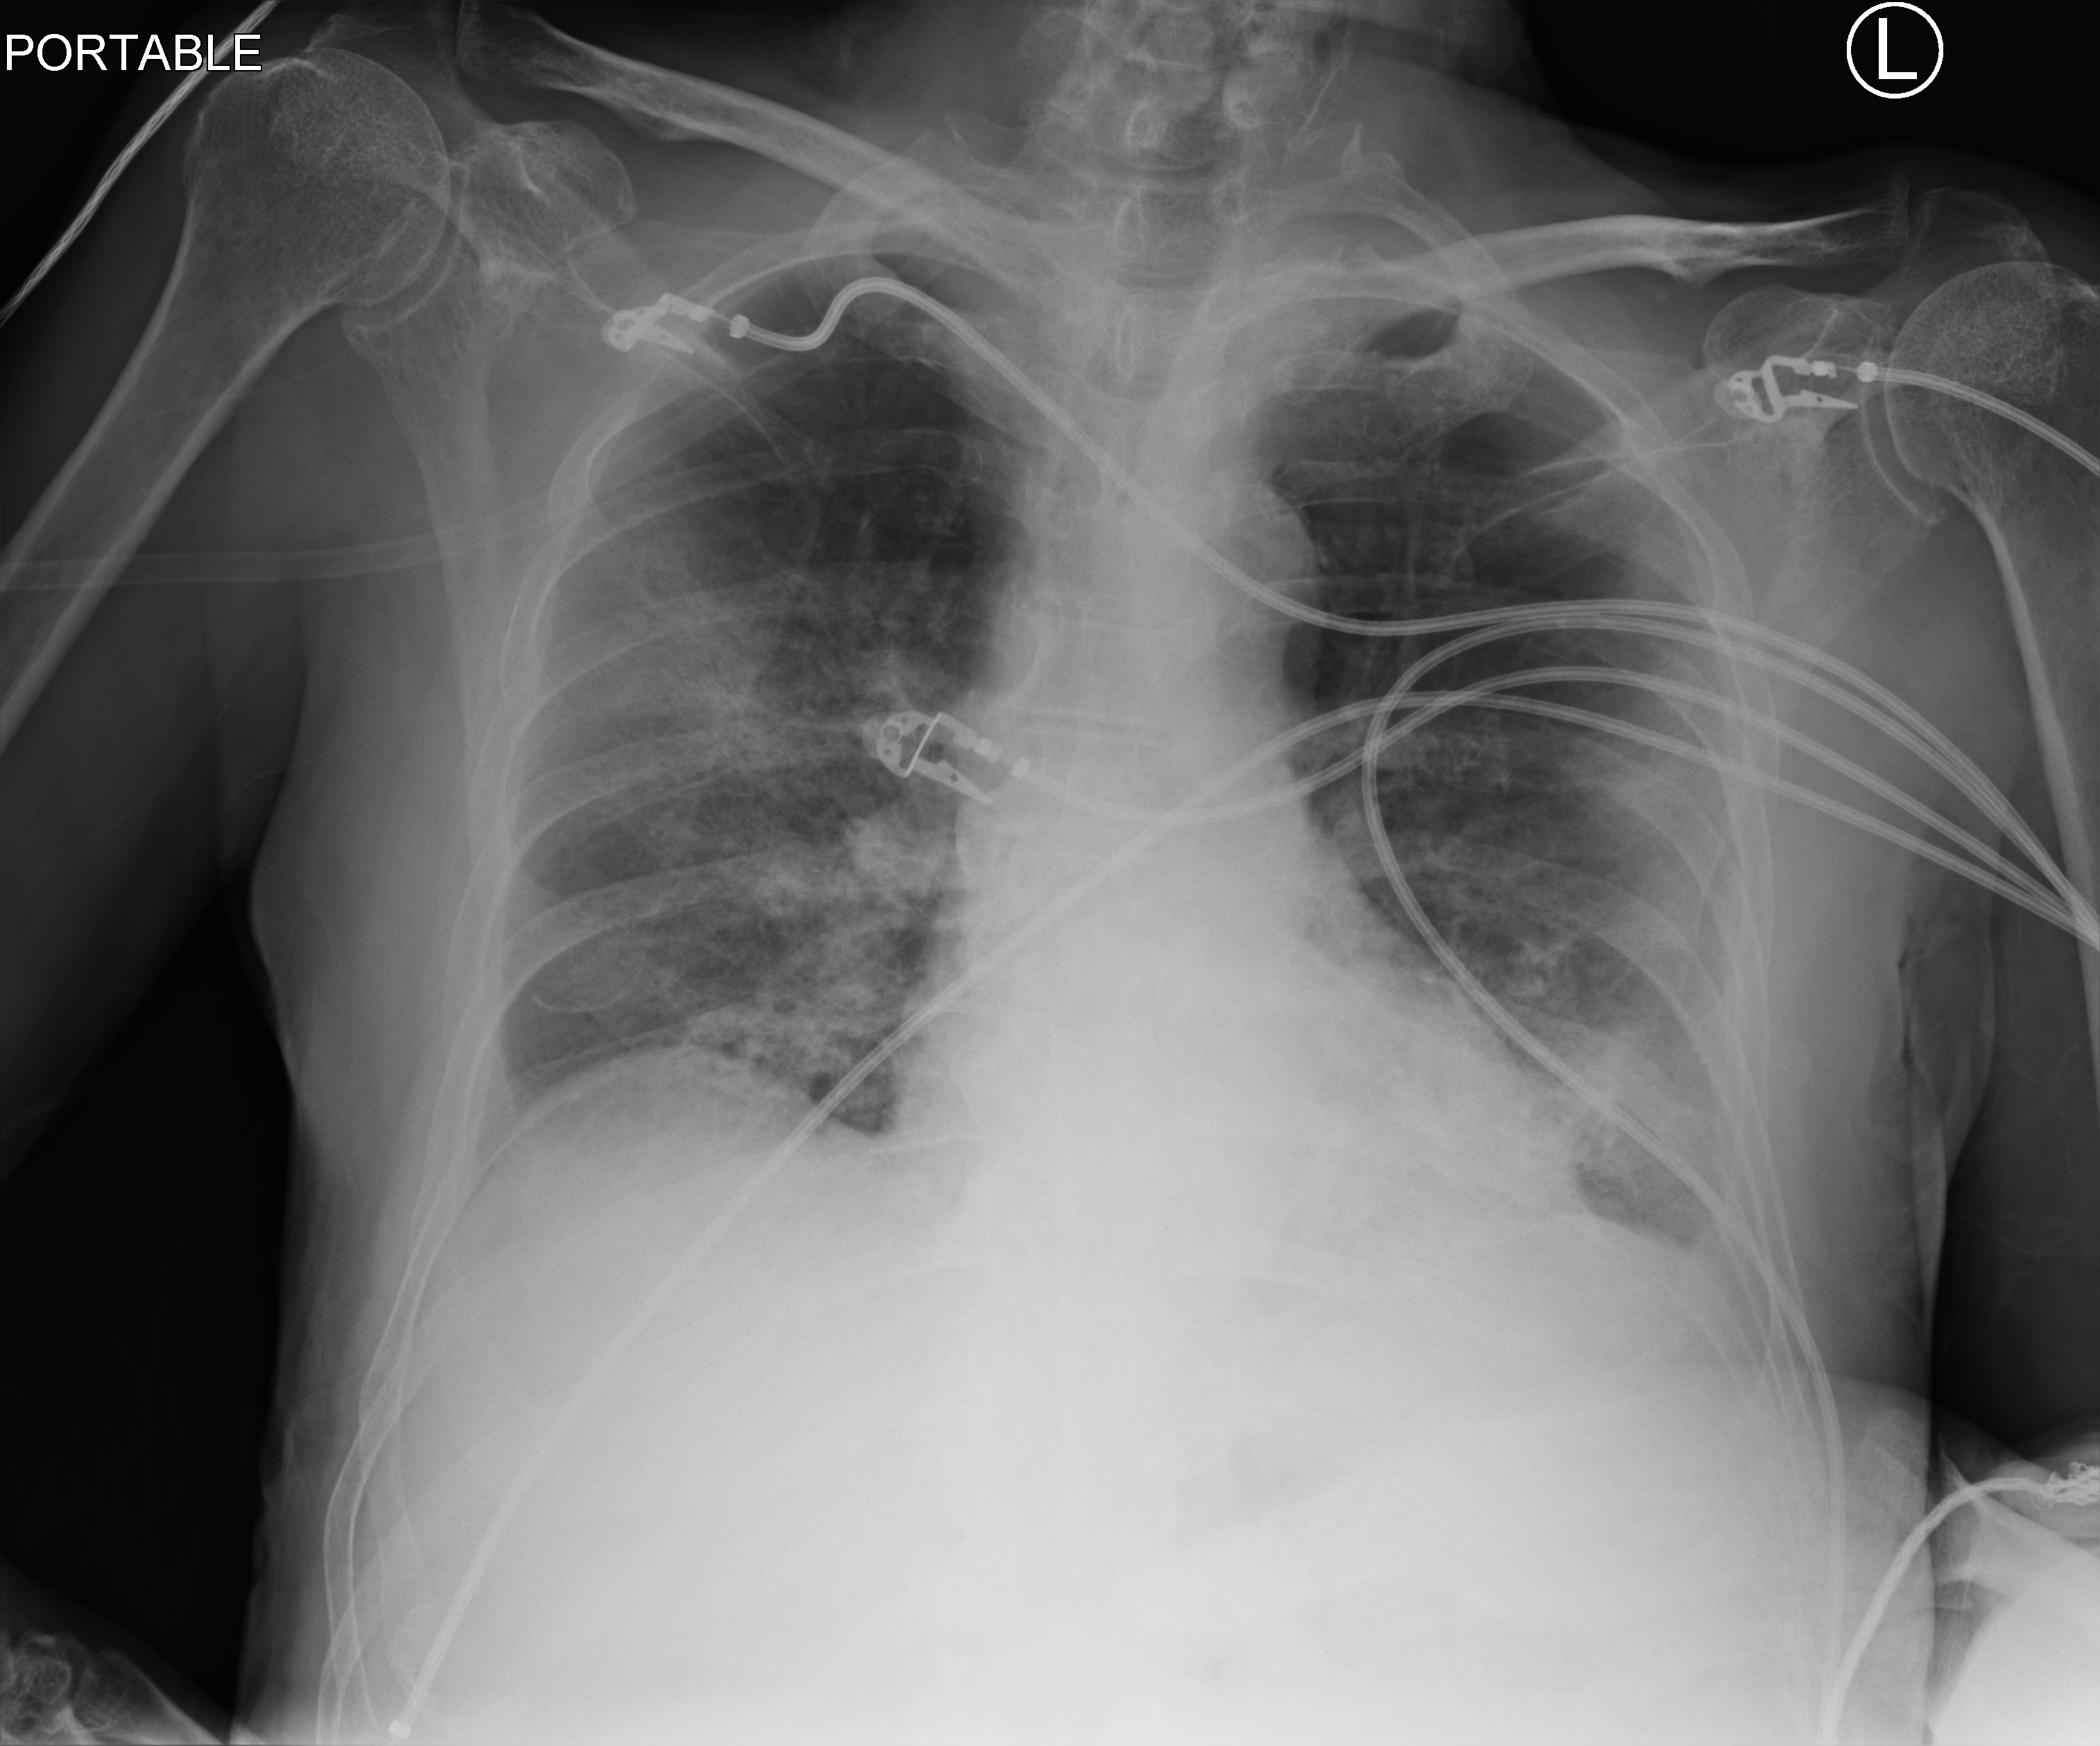
Portable chest radiograph; anteroposterior (AP) projection. Patient hospitalised with COVID-19; male, aged 60–74 years.
Admission-level facts for this patient (not findings on this image; timing relative to this image not recorded):
- length of hospital stay: 42 days
- admitted to intensive care during this hospital stay: yes
- mechanically ventilated during this hospital stay: yes